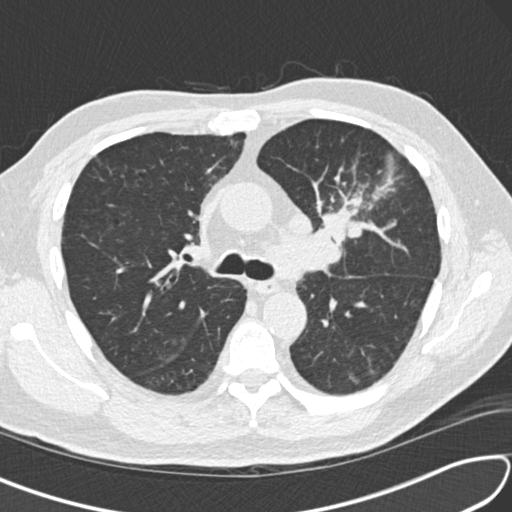
Low-dose screening chest CT, one axial slice; reconstruction kernel B30f; 120 kVp; lung window (W 1500 / L -600 HU); 2 mm slice thickness; 512 × 512 image matrix, field of view 340 × 340 mm.
Structures marked on this image (outlined manually by an expert reader):
- lesion 1 (tumor, upper lobe of left lung): box from (x=324, y=208) to (x=363, y=243) px